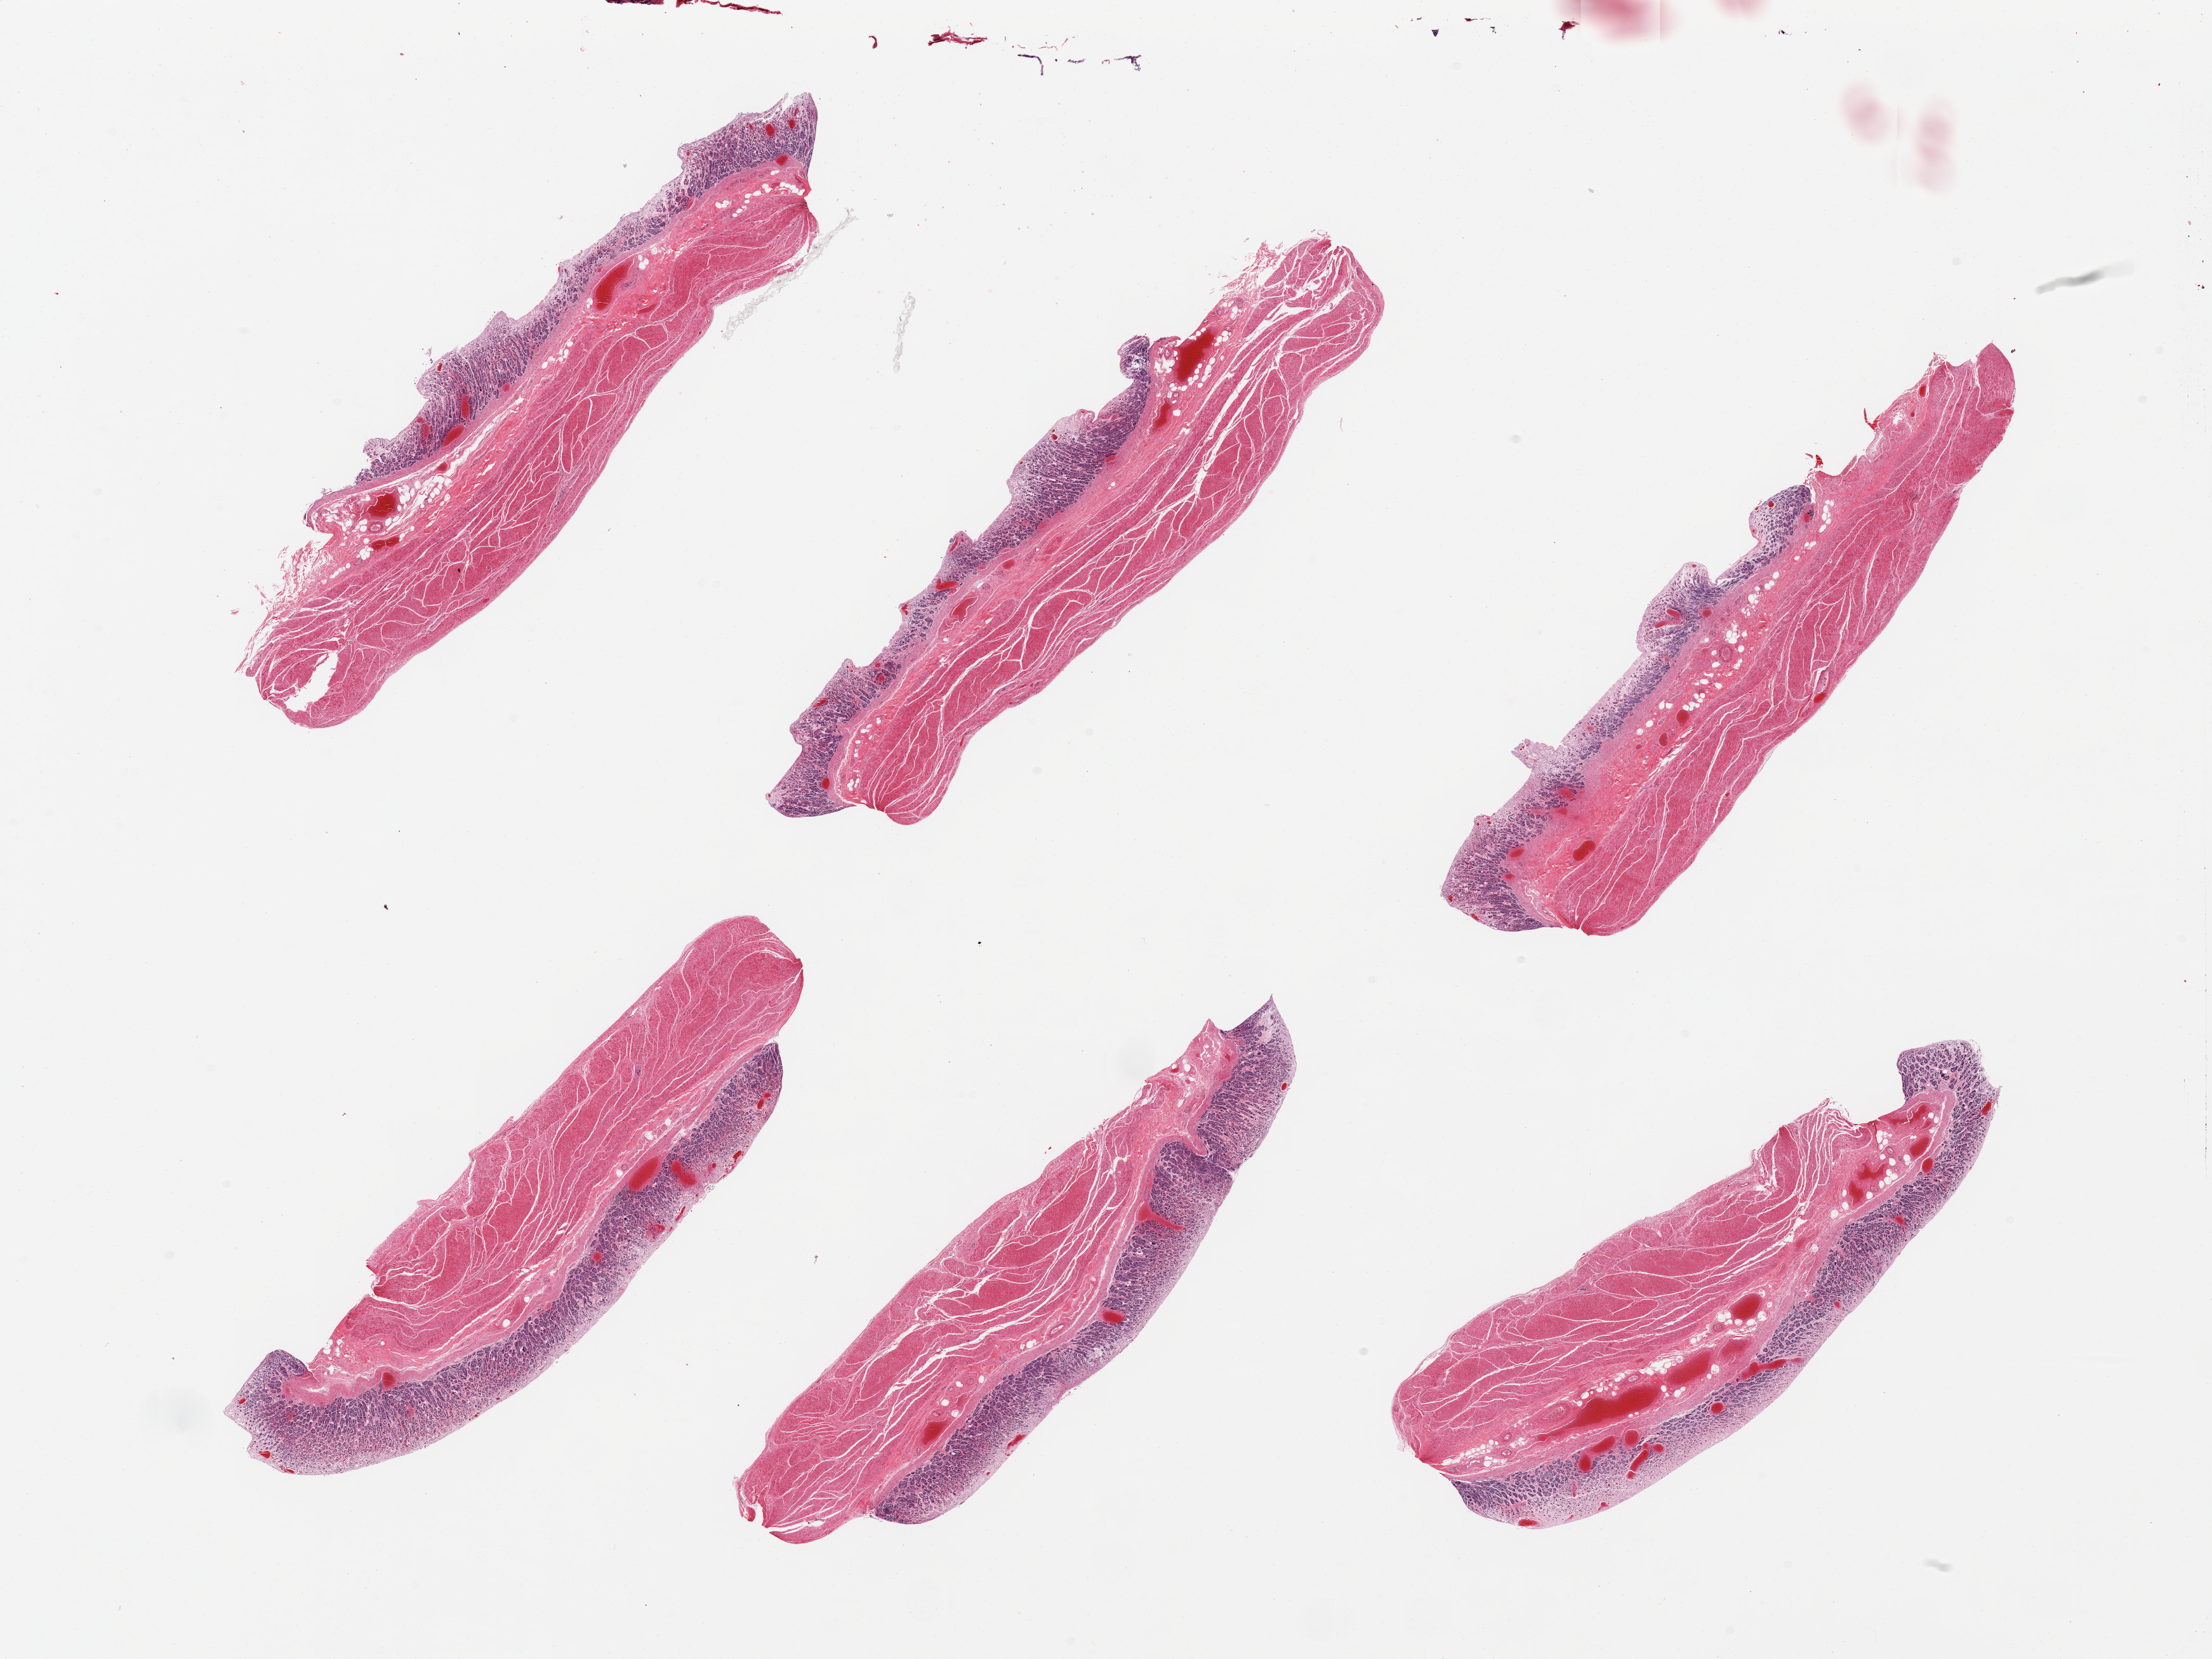
Hematoxylin and eosin (H&E) whole-slide image, brightfield, whole scanned area (about 27.6 x 20.7 mm, acquisition: 20x scan) shown as a low-resolution overview. PAXgene-fixed, paraffin-embedded tissue. Sampled site (target tissue): stomach. Tissue donor sample.
• reviewer comment on this tissue sample: 6 pieces; epithelium largely autolyzed; full thickness present